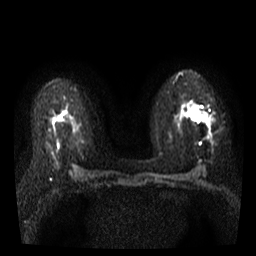
Breast MRI, one axial slice. Position 19 of 35 along the scan axis. Diffusion-weighted series; image 2 of 4 stored at this slice position (different b-values; order by instance number). 3 T. 256 × 256 image matrix, field of view 300 × 300 mm. Female patient.
Outlined on this slice (manually delineated by an expert):
- tumour on diffusion-weighted imaging: bounding box (x1, y1, x2, y2) in pixels: (194, 111, 207, 120)